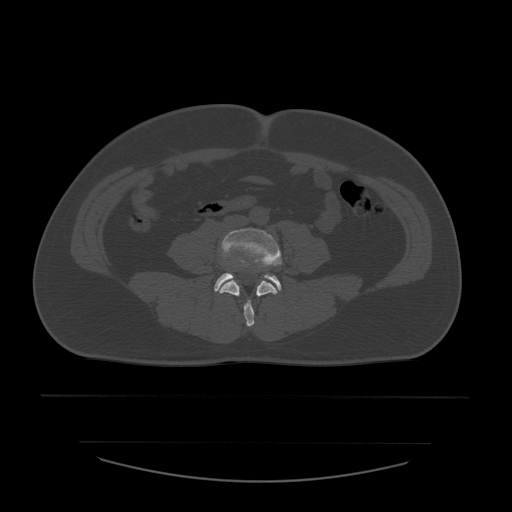
CT including the spine, one axial slice. Position 137 of 532 along the scan axis. Reconstruction kernel STANDARD. Bone window (W 1800 / L 400 HU). 512 × 512 image matrix, field of view 441 × 441 mm. Patient age 44 years. From the clinical record (not read from this slice): primary cancer: soft tissue sarcoma.
Annotated regions visible in this slice (semi-automatically segmented with operator editing):
- L4 vertebra: bounding box (x1, y1, x2, y2) in pixels: (218, 229, 282, 327)
- L5 vertebra: (215, 273, 282, 292)